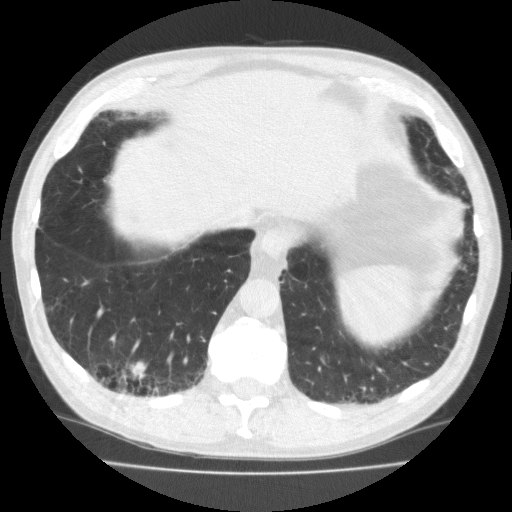
Axial slice from a low-dose chest CT screening exam; second annual screen; lung window (W 1500 / L -600 HU); 2 mm slice thickness; 120 kVp; slice 144 of 195 in the series. Male participant, aged 70 years at enrolment.
Expert-annotated lung lesion, box from (x=97, y=344) to (x=160, y=397) px. The exam's reader record, not a measurement of the box and not confirmed to be the same lesion: non-calcified nodule or mass ≥4 mm, right lower lobe, 18 × 13 mm, spiculated (stellate) margins, soft tissue attenuation, pre-existing on the prior screen: no. Lung cancer was diagnosed 64 days after this screen: squamous cell carcinoma, NOS, right lower lobe, moderately differentiated (G2), stage IA (AJCC 6th edition), 20 mm at pathology.